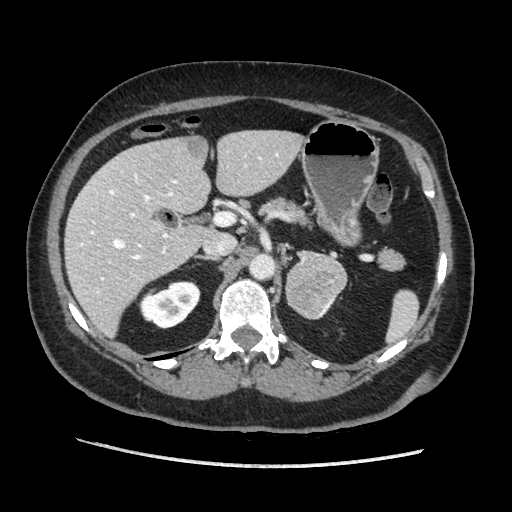
Contrast-enhanced abdominal CT, one axial slice; position 121 of 203 along the scan axis; soft-tissue window (W 400 / L 40 HU); 1.25 mm slice thickness; 512 × 512 image matrix, field of view 360 × 360 mm. Female patient. From the clinical record (not read from this slice): diagnosis: adrenocortical carcinoma; tumour side: left adrenal; tumour size at pathology: 6.5 cm; Ki-67 index: 22 %; stage (as recorded): 2.
Outlined on this slice (semi-automatically segmented with operator editing):
- mass: bounding box (x1, y1, x2, y2) in pixels: (287, 254, 349, 319)